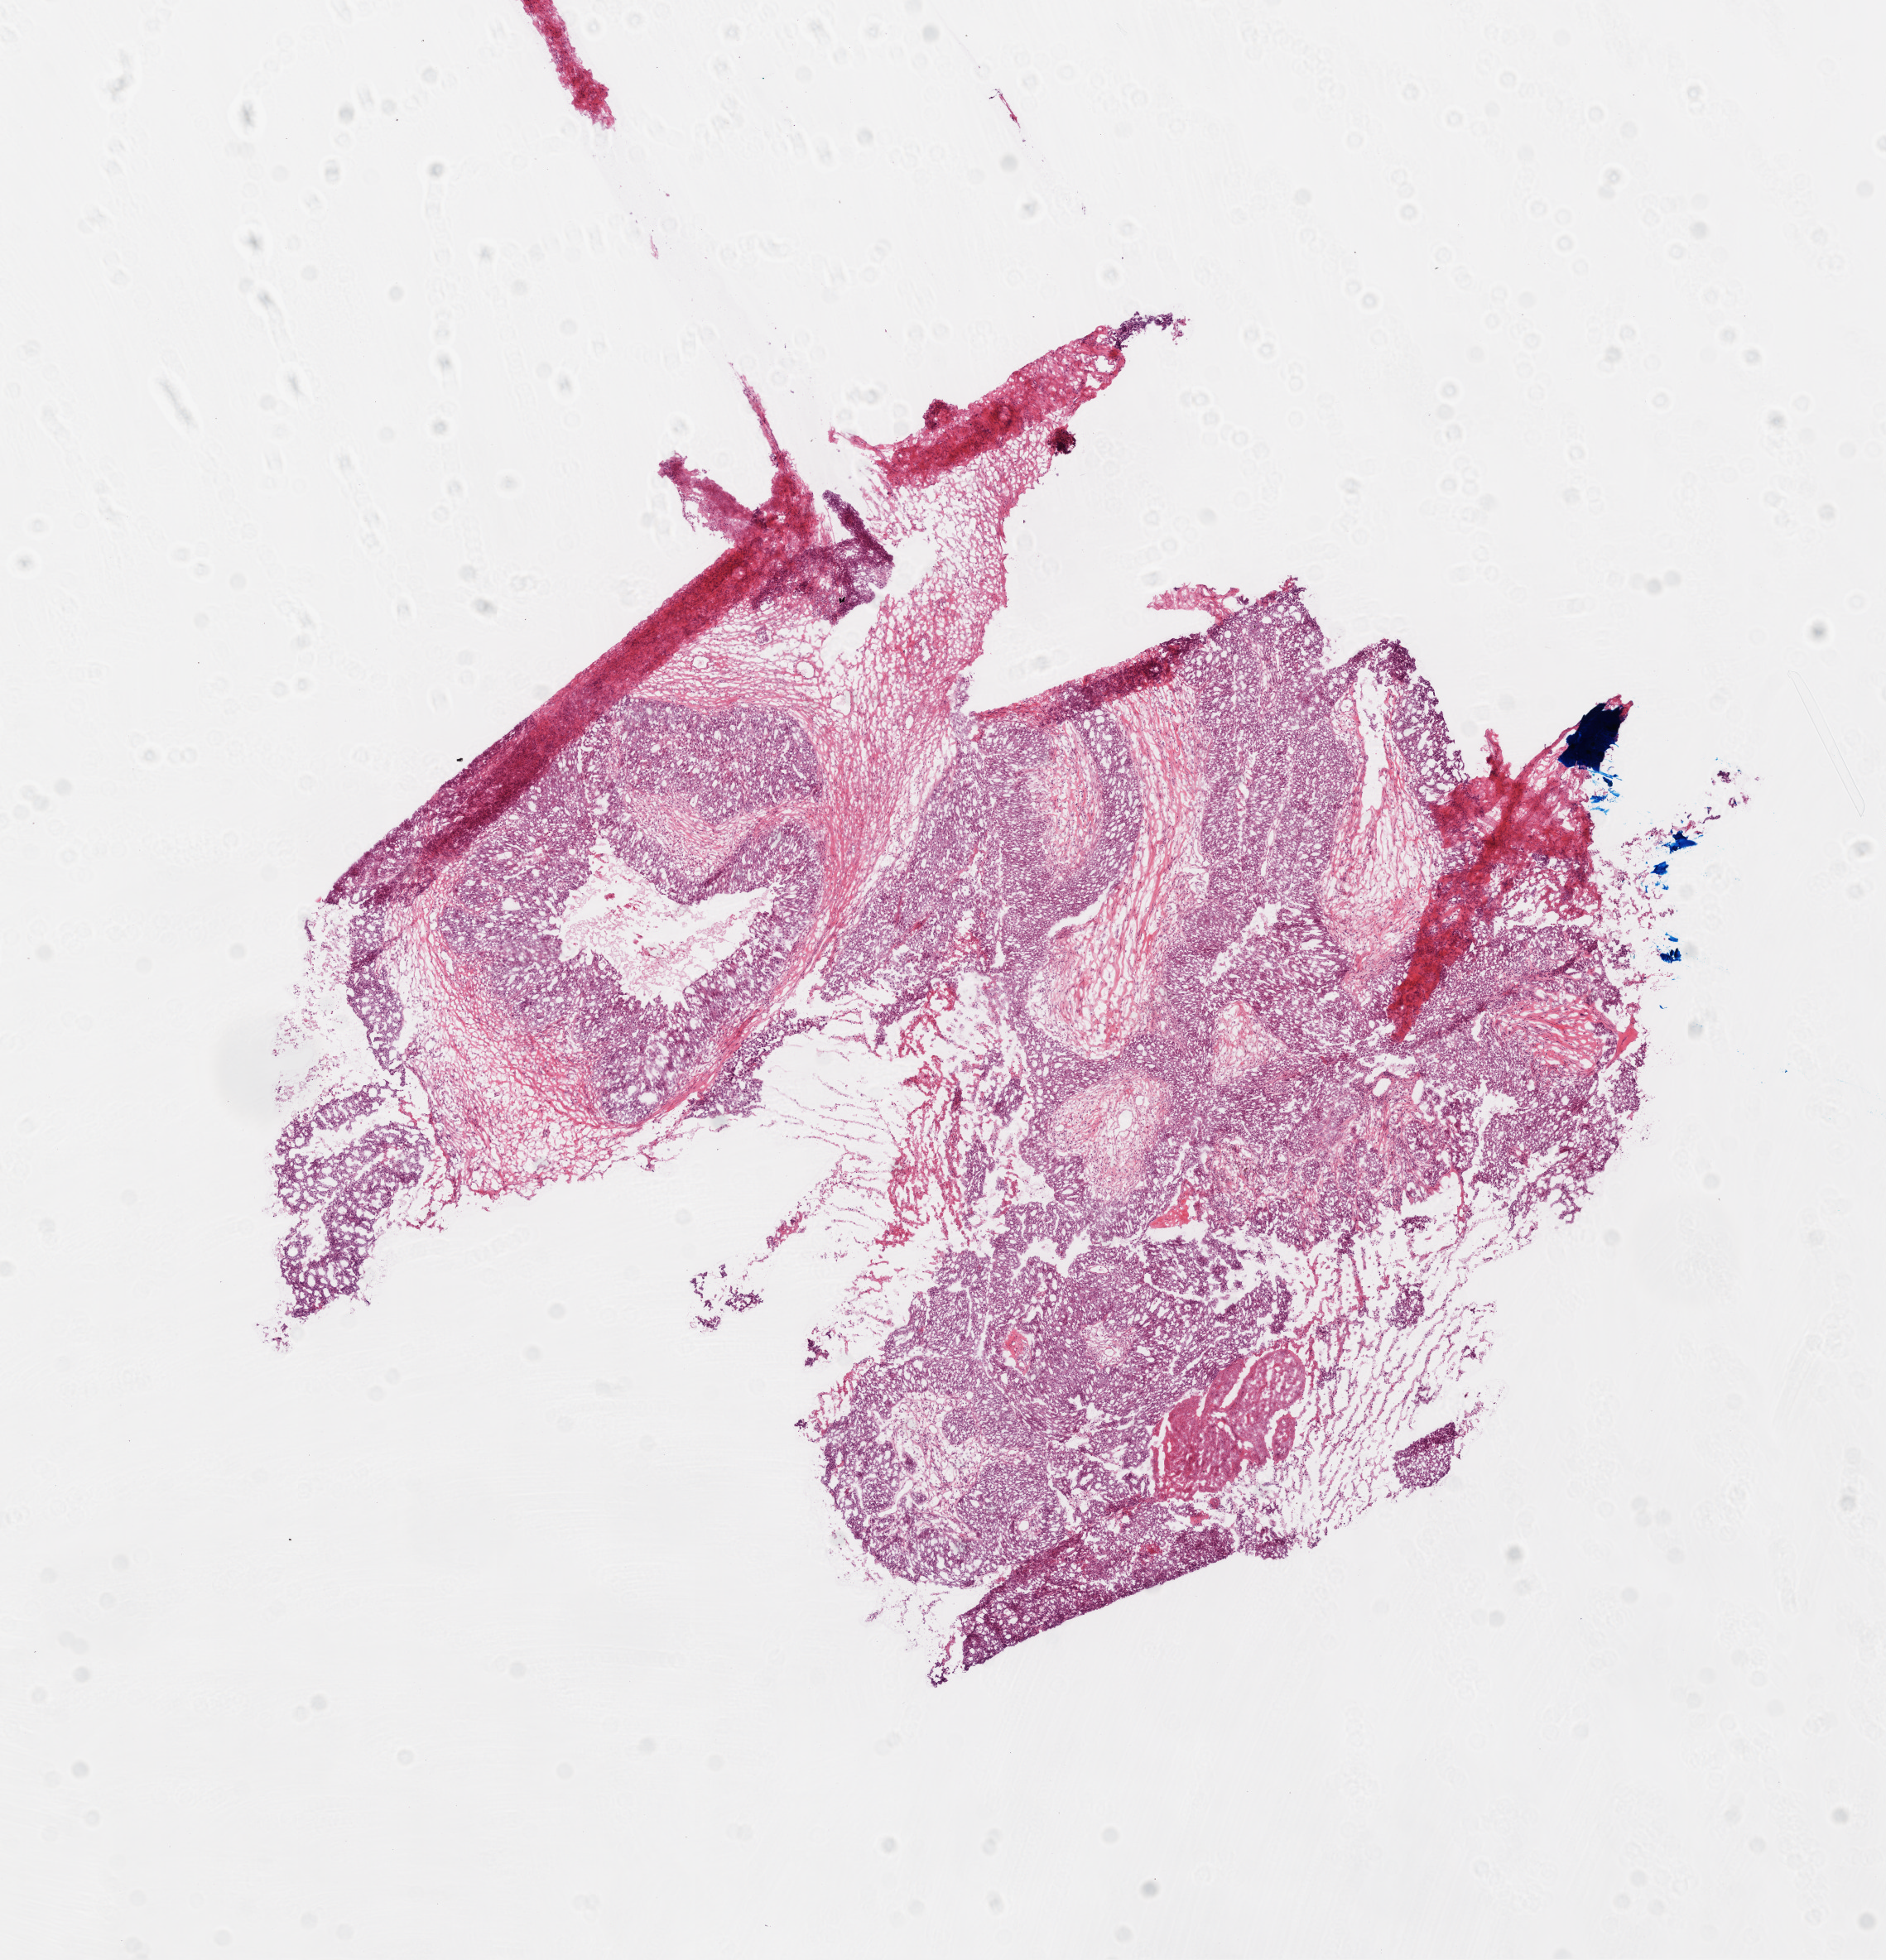
Hematoxylin and eosin (H&E) stained whole-slide image, low-resolution overview of the scanned area, about 9.2 x 9.5 mm, frozen section, sample: primary tumour, ovary. Female, age 43 years at initial diagnosis. Histologic grade: G3 (poorly differentiated). Slide review estimates, as recorded: tumour cells 75%, tumour nuclei 80%, normal cells 10%, stromal cells 10%, necrosis 5%.
Histologic diagnosis: Serous cystadenocarcinoma, NOS. FIGO stage: IIIC.